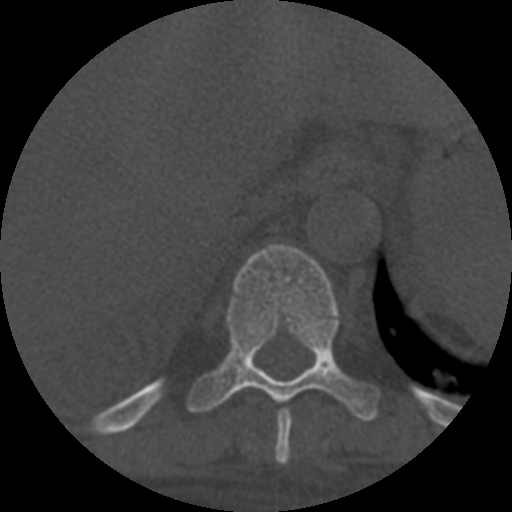
CT including the spine, one axial slice. Slice 360 of 708 in the series (ordered by position). Reconstruction kernel STANDARD. 120 kVp. One of 3 acquisitions stored at this slice position. Bone window (W 1800 / L 400 HU). 1.25 mm slice thickness. 512 × 512 image matrix, field of view 160 × 160 mm. Patient age 55 years. Case-level facts recorded for this patient, not image findings: primary cancer: colon; vertebrae with lytic lesions (as recorded): T12, L1, L5.
Structures marked on this image (semi-automatically segmented with operator editing):
- T10 vertebra: bounding box [x1, y1, x2, y2] px = [187, 244, 381, 421]
- T9 vertebra: [275, 409, 292, 464]